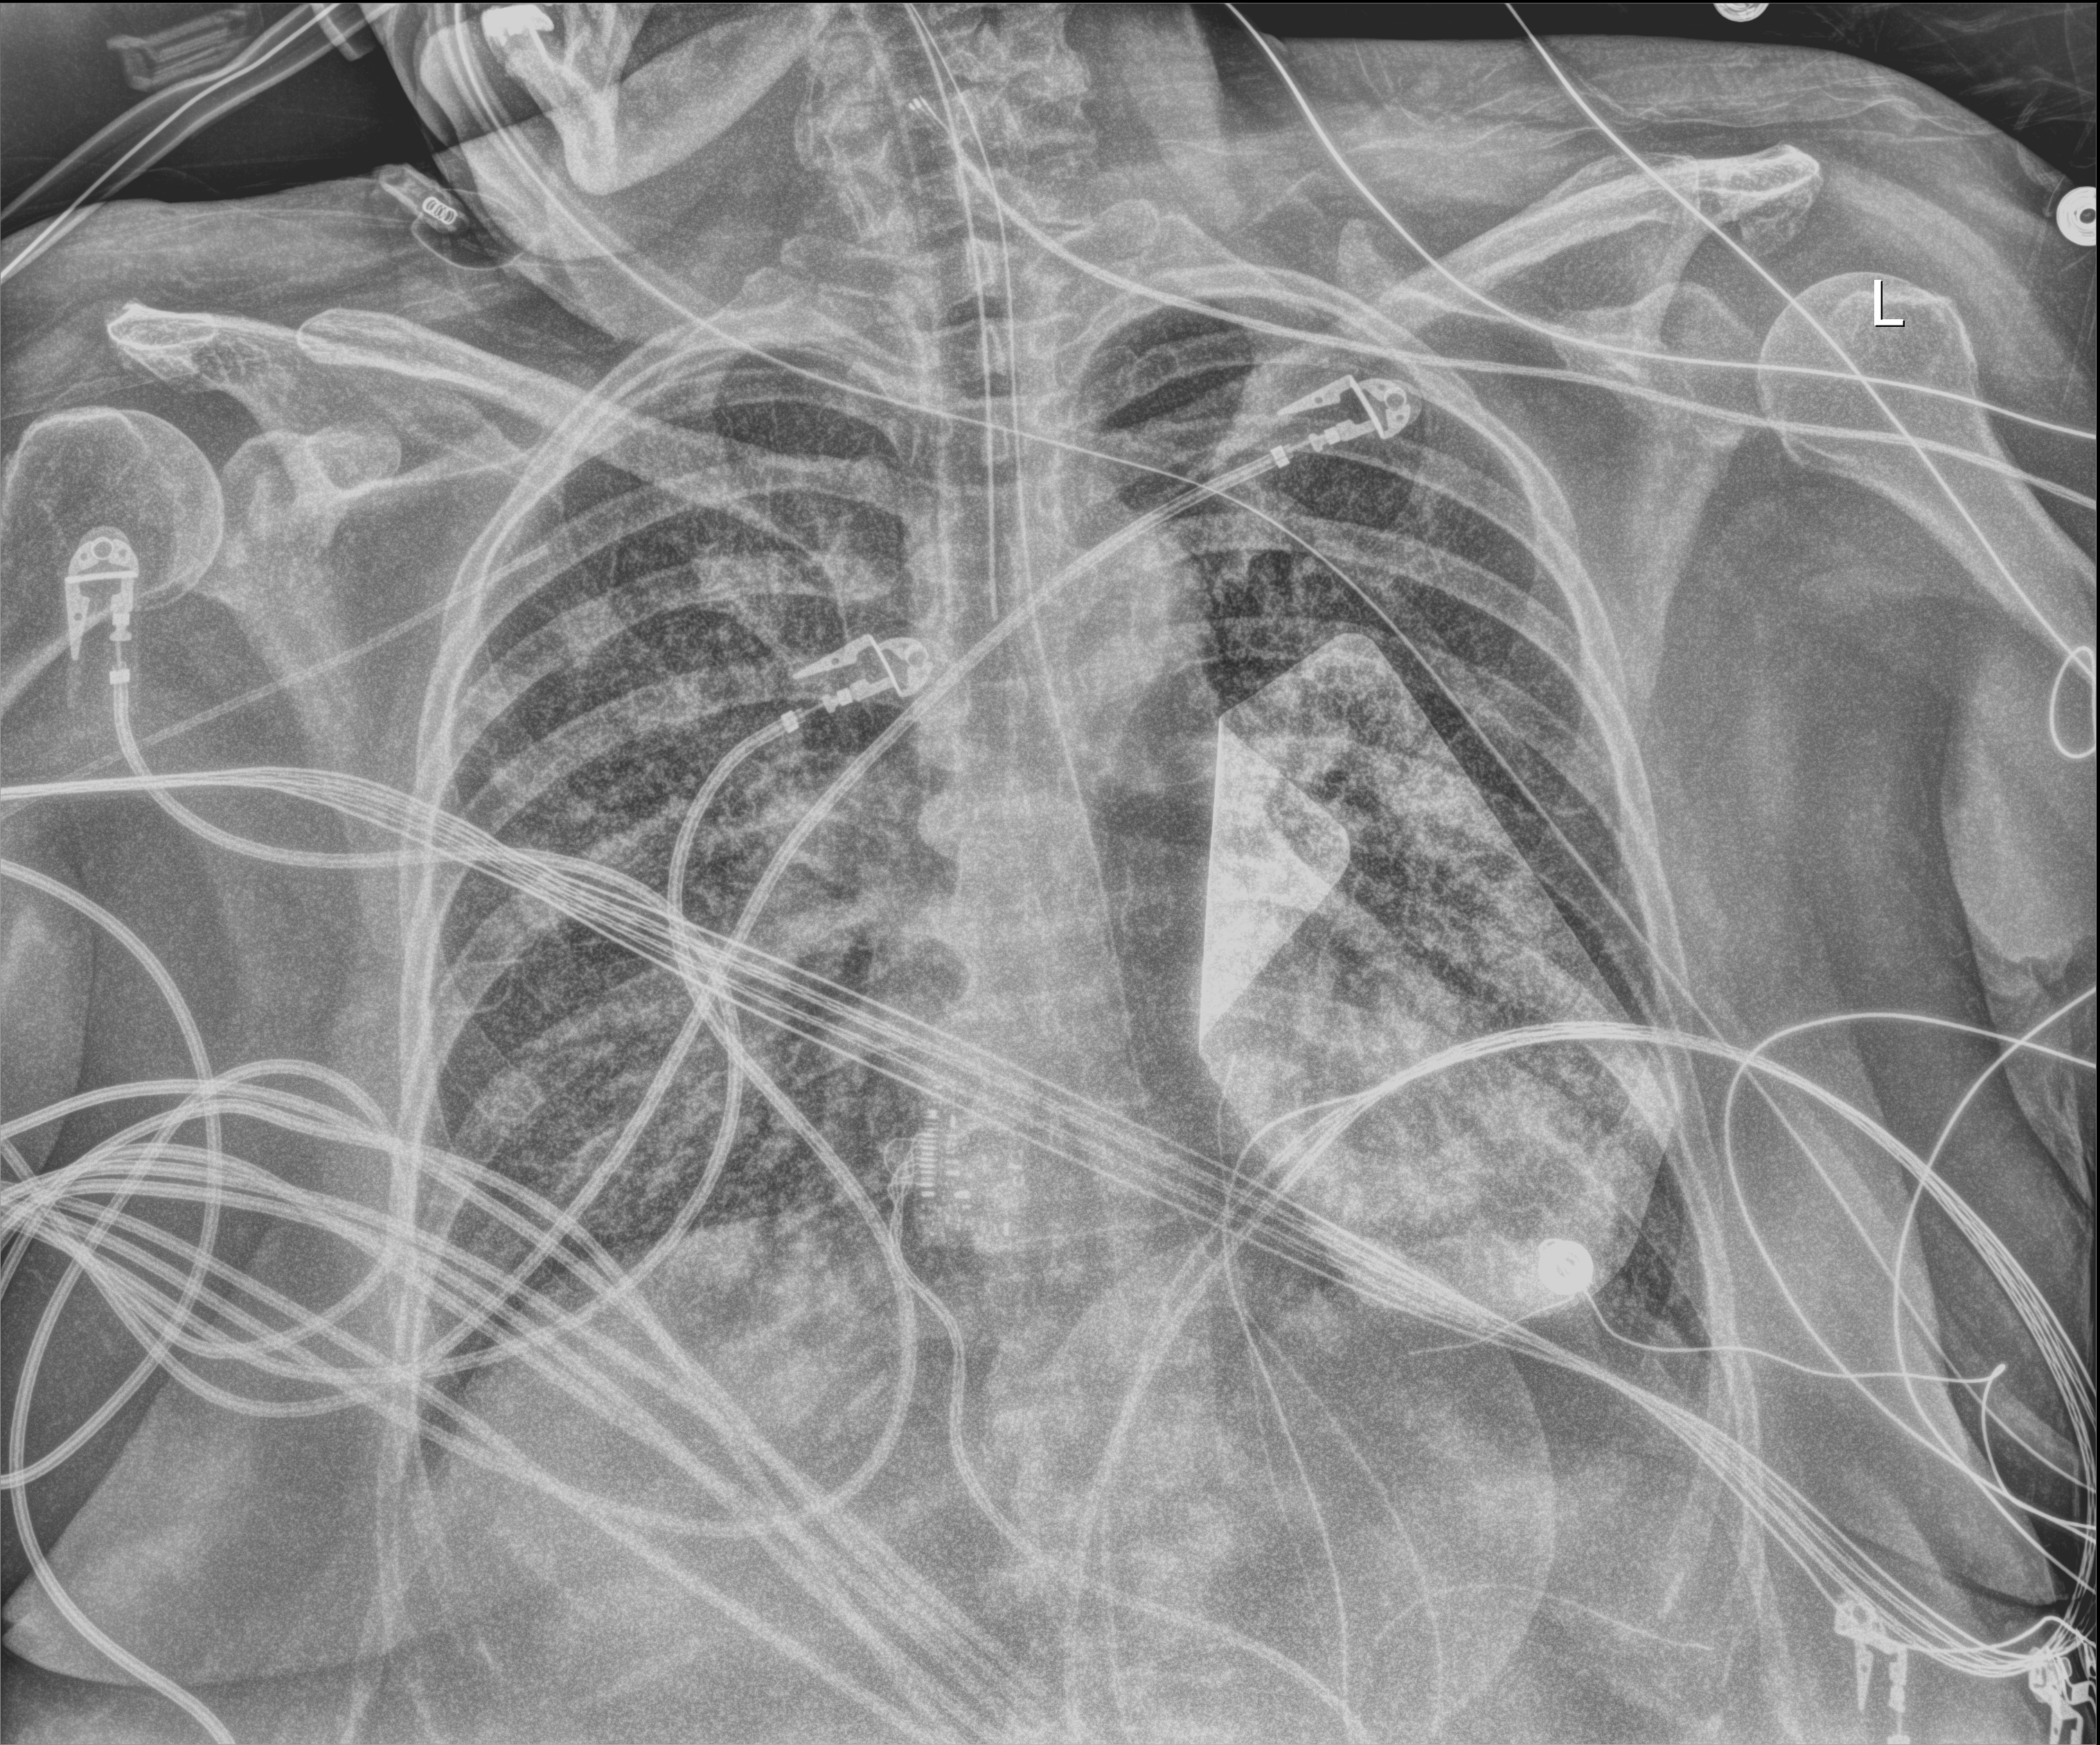
Chest radiograph. Patient hospitalised with COVID-19; female, aged 60–74 years.
Admission-level facts for this patient (not findings on this image; timing relative to this image not recorded): diabetes (admission record): no.